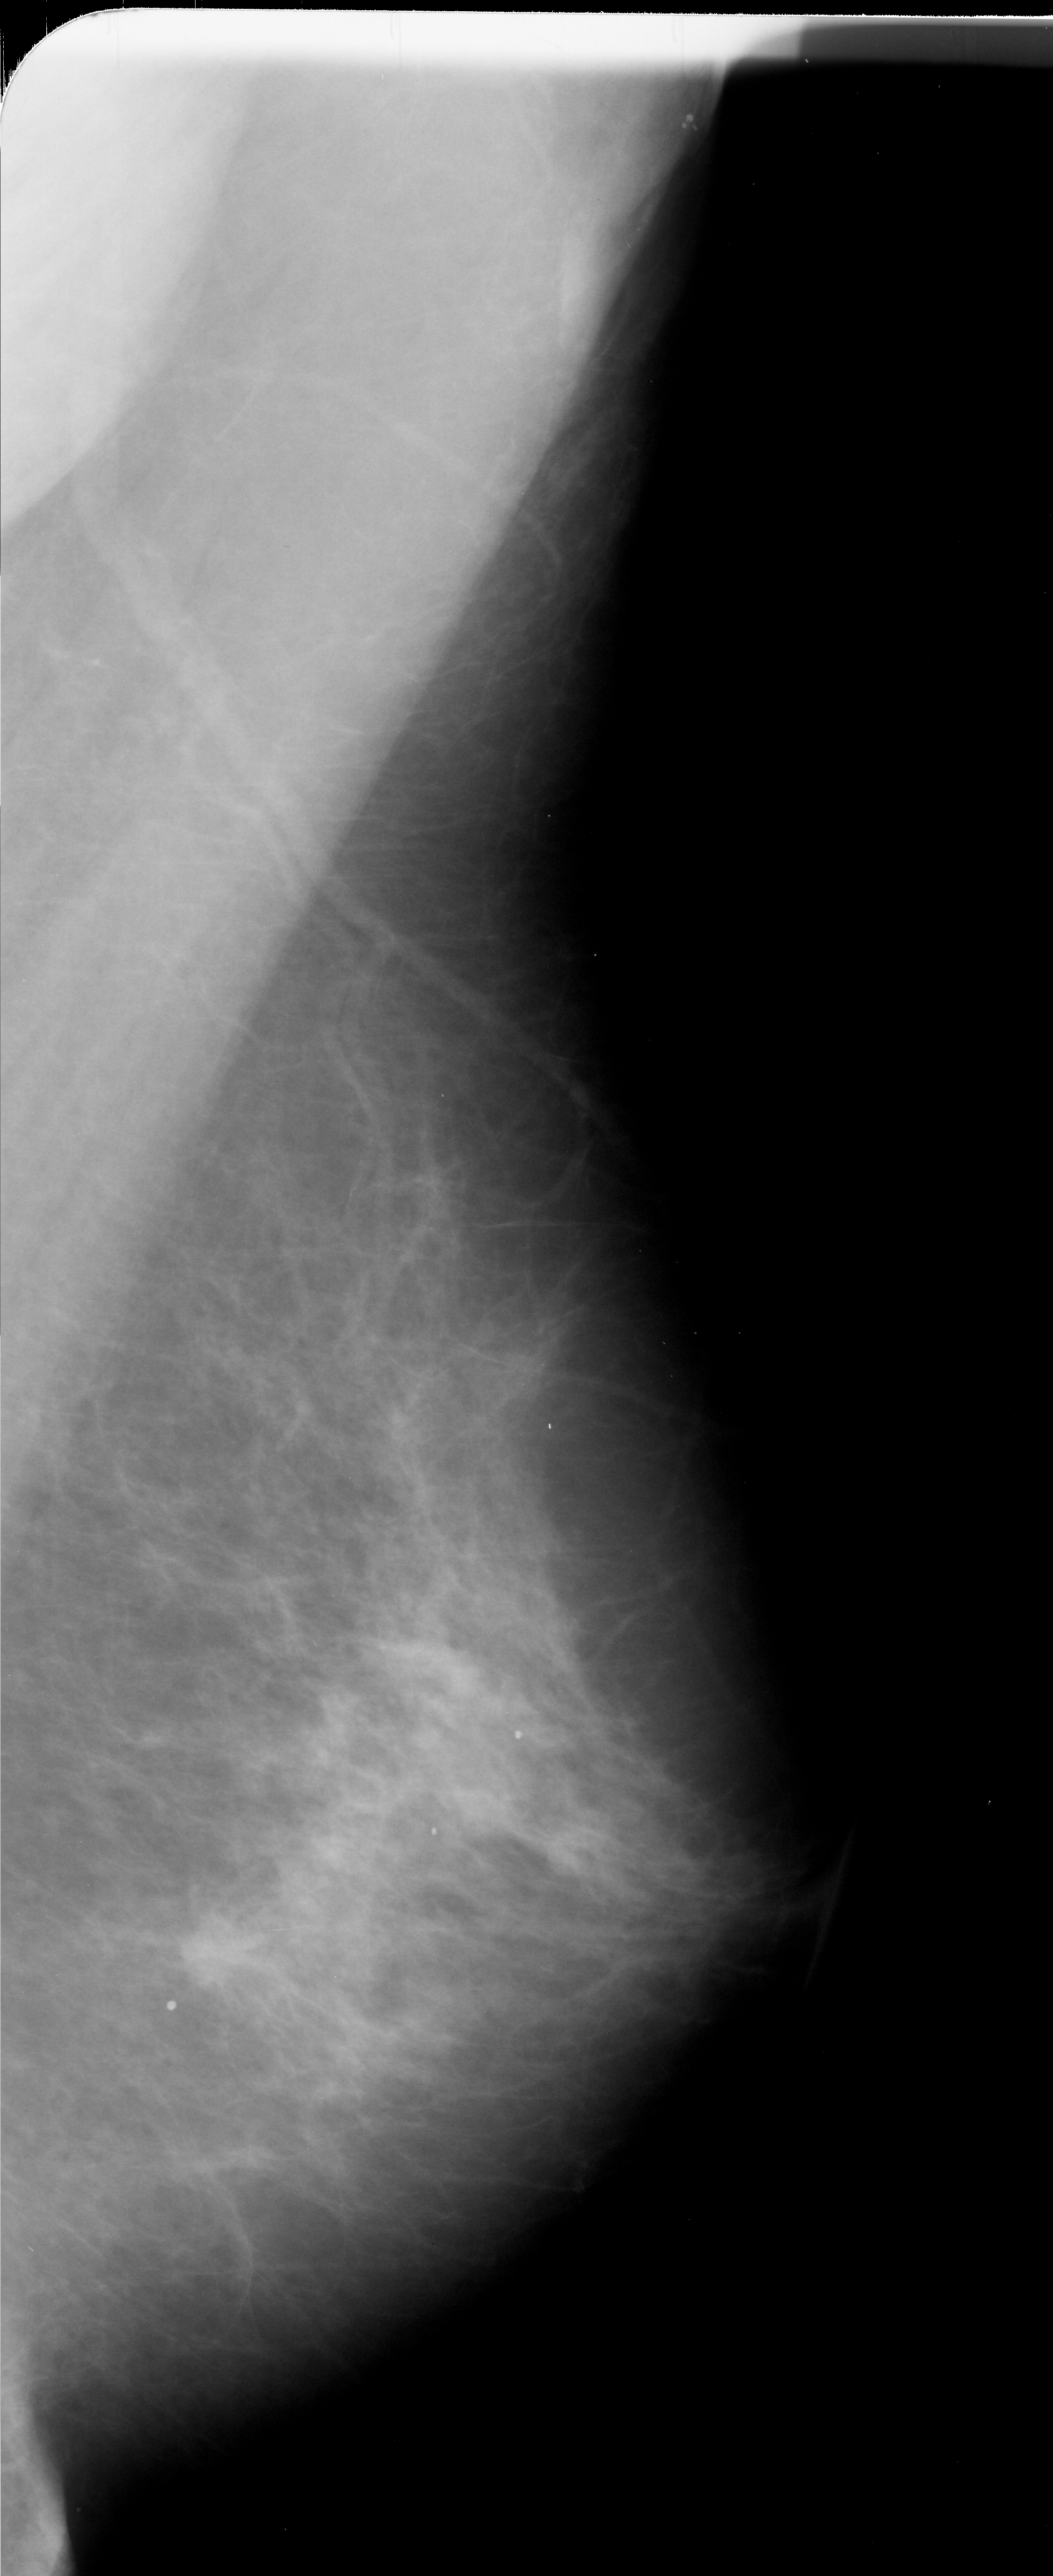
Digitized screen-film mammogram; right breast; mediolateral oblique (MLO) view; BI-RADS breast density category 3 (scale 1–4).
- Mass, shape lobulated, margins ill defined; BI-RADS assessment category 4; subtlety rating 4 on a 1 (subtle) to 5 (obvious) scale; pathology result (as recorded, not read from the image): malignant.